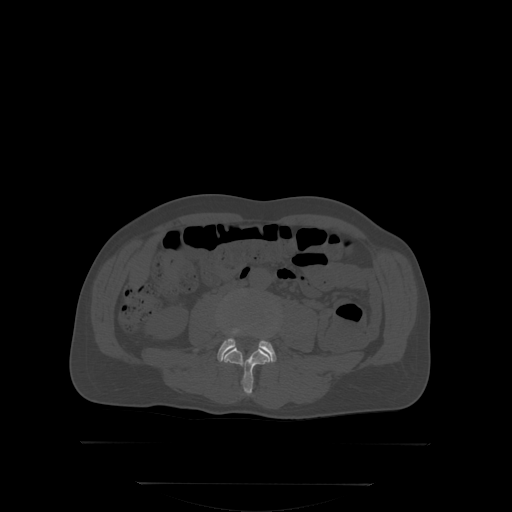
CT including the spine, one axial slice. Position 116 of 350 along the scan axis. Bone window (W 1800 / L 400 HU). 512 × 512 image matrix, field of view 500 × 500 mm. Male patient, age 58 years. Case-level facts recorded for this patient, not image findings: primary cancer: prostate; vertebrae with lytic lesions (as recorded): L1.
Structures marked on this image (semi-automatic segmentation, software-assisted and operator-edited):
- L3 vertebra: box from (x=225, y=347) to (x=270, y=395) px
- L4 vertebra: (x=218, y=330)–(x=276, y=361)